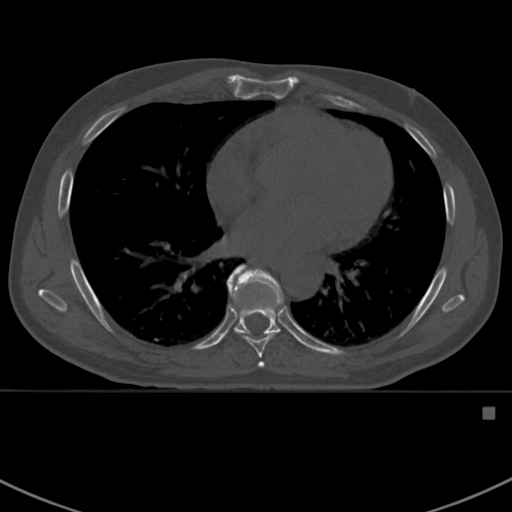
CT including the spine, one axial slice. Position 409 of 412 along the scan axis. 120 kVp. Bone window (W 1800 / L 400 HU). 1.5 mm slice thickness. 512 × 512 image matrix, field of view 358 × 358 mm. Patient: male, 59 years. Case-level facts recorded for this patient, not image findings: primary cancer: prostate.
Structures marked on this image (semi-automatically segmented with operator editing):
- T7 vertebra: bounding box <228,282,276,368> (left, top, right, bottom; pixels)
- T8 vertebra: <227,264,283,338>